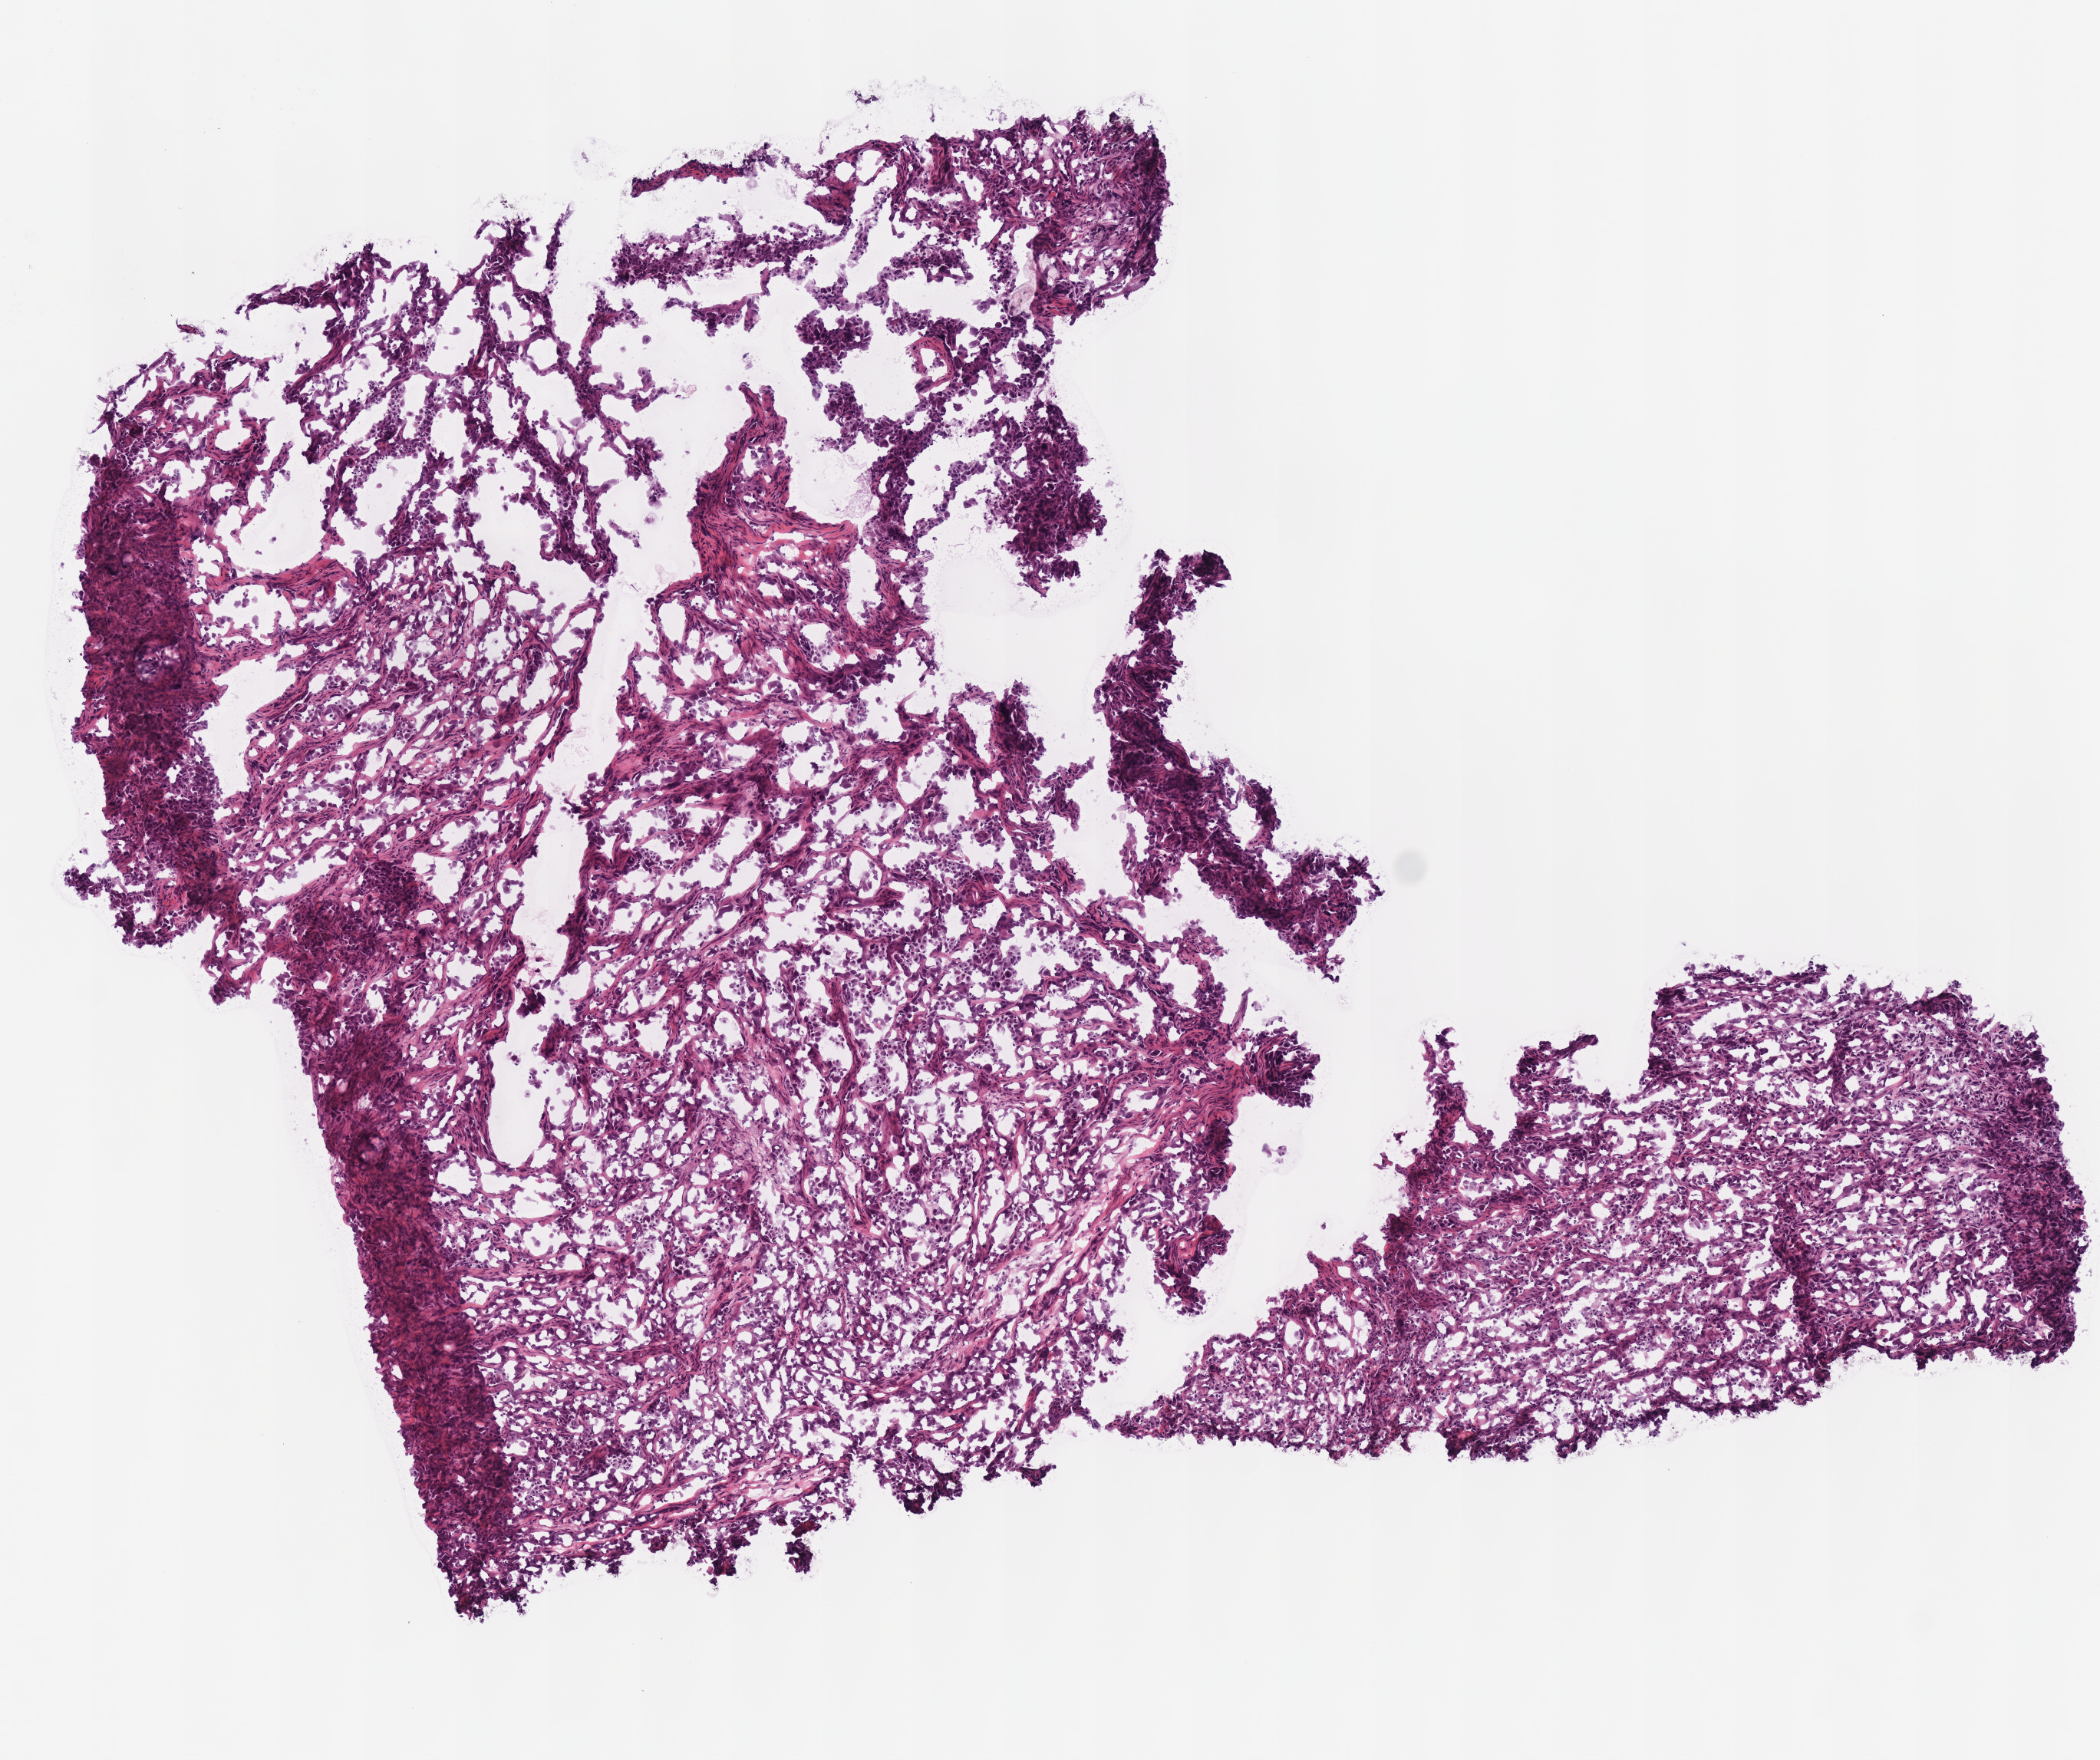
Digitized Hematoxylin and eosin (H&E) stained tissue section (whole slide), low-resolution overview of the scanned area, about 5.4 x 4.5 mm (acquisition: 40x scan), frozen section from the top of the tissue portion, primary tumour sample from the head and neck. Male, age 55 years at initial diagnosis. Histologic grade: G3 (poorly differentiated). Composition of this section per pathologist review: tumour cells 100%, tumour nuclei 61%, normal cells 0%, stromal cells 0%, necrosis 0%. Infiltration values recorded for this section: lymphocyte infiltration 10%, monocyte infiltration 0%, neutrophil infiltration 0%.
* AJCC pathologic stage: IVA (7th edition)
* lymph nodes positive (case pathology): 14 of 24 examined
* diagnosis: Squamous cell carcinoma, NOS (overlapping lesion of lip, oral cavity and pharynx)